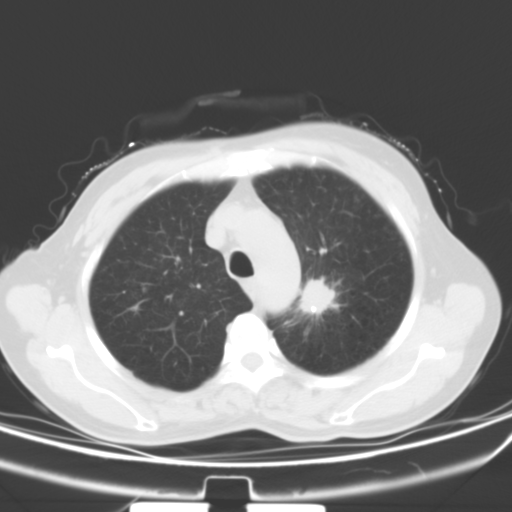
Chest CT, one axial slice; position 44 of 53 along the scan axis; 120 kVp; lung window (W 1500 / L -600 HU); 5 mm slice thickness; 512 × 512 image matrix. Female patient, age 60 years. Case-level facts recorded for this patient, not image findings: clinical TNM (as recorded): T1b N0 M0.
Annotated regions visible in this slice (bounding box drawn by a radiologist):
- lung tumour (recorded histology: squamous cell carcinoma): bounding box <290,277,345,330> (left, top, right, bottom; pixels)